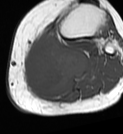
MRI of an extremity soft-tissue mass, one axial slice. Slice 39 of 68 in the series (ordered by position). MR volume resampled by the dataset authors to the PET/CT grid (not the native acquisition matrix). 123 × 134 image matrix, field of view 120 × 131 mm. Female patient. Case-level facts recorded for this patient, not image findings: histological type: extraskeletal high grade osteogenic sarcoma; grade: high; site of the primary tumour: left calf.
Annotated regions visible in this slice (expert contour drawn on MRI and transferred to this co-registered scan by the dataset authors):
- gross tumour volume (mass): box from (x=24, y=32) to (x=89, y=95) px